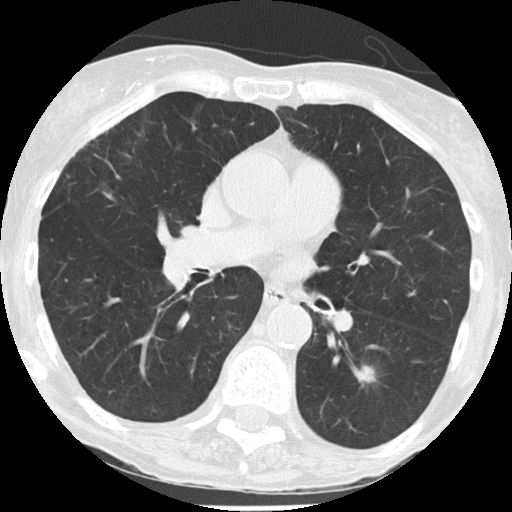
Low-dose screening chest CT, one axial slice. Position 70 of 146 along the scan axis. 120 kVp. Lung window (W 1500 / L -600 HU). 2 mm slice thickness. 512 × 512 image matrix, field of view 273 × 273 mm.
Structures marked on this image (expert manual segmentation):
- lesion 1 (tumor, lower lobe of left lung): box from (x=360, y=366) to (x=375, y=382) px